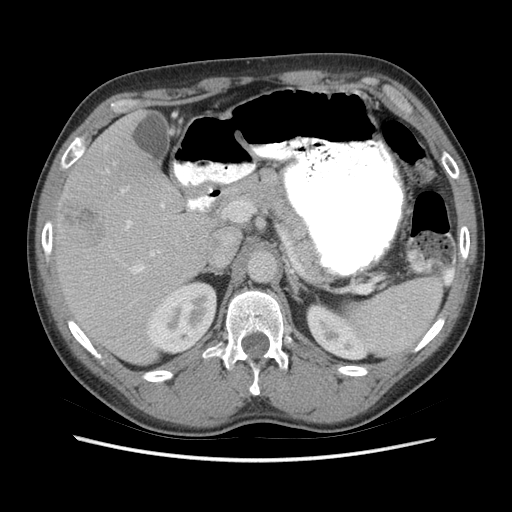
Contrast-enhanced abdominal CT (liver protocol), one axial slice; slice 36 of 73 in the series (ordered by position); soft-tissue window (W 400 / L 40 HU); 2.5 mm slice thickness; 512 × 512 image matrix, field of view 360 × 360 mm. From the clinical record (not read from this slice): diagnosis: hepatocellular carcinoma (patient treated with transarterial chemoembolisation; whether this scan precedes or follows treatment is not stated here); TNM stage (as recorded): Stage-IIIA; Child-Pugh class: A; tumour nodularity: multinodular.
Annotated regions visible in this slice (semi-automatic segmentation, software-assisted and operator-edited):
- liver parenchyma outside the tumour (the mass and vessels are separate outlines, so this box may not span the whole liver): bounding box <54,110,240,364> (left, top, right, bottom; pixels)
- mass: <61,202,107,252>
- liver vessels: <121,189,231,274>